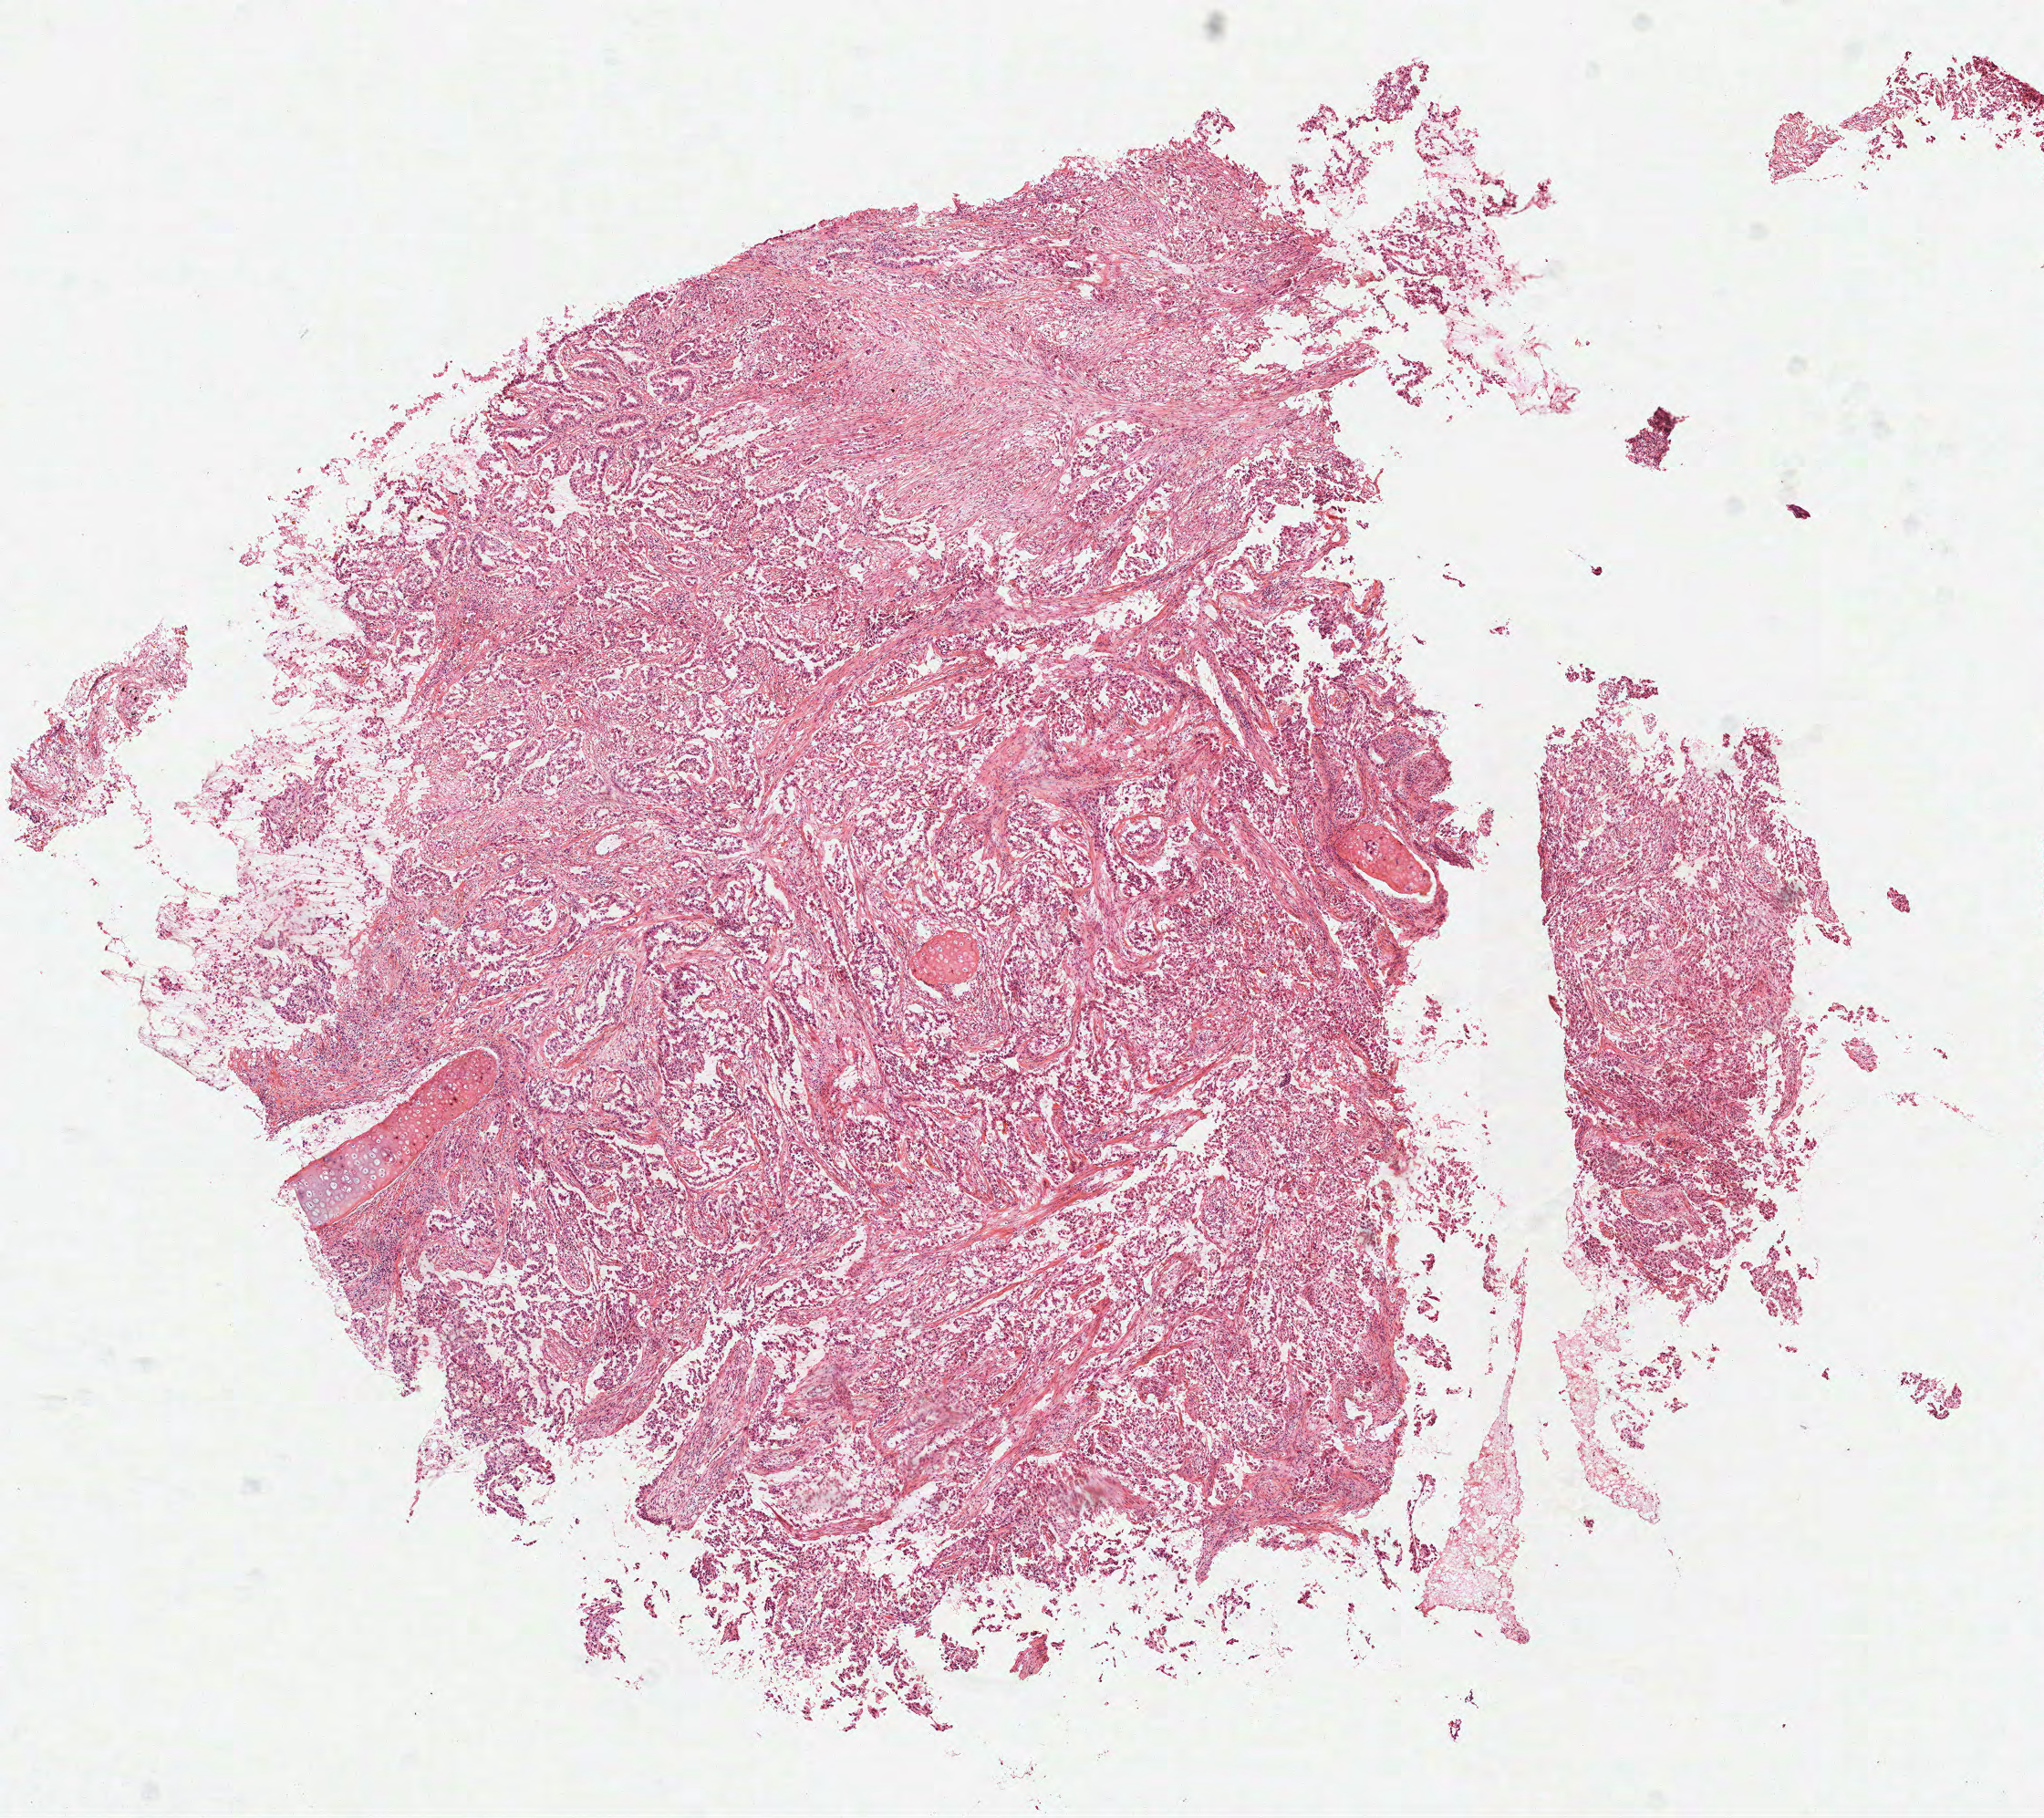
Whole-slide histology image, Hematoxylin and eosin (H&E) stained, a low-resolution overview of the entire scanned area, about 9.0 x 8.0 mm, frozen section, sample: primary tumour, lung. Female, age 60 years at initial diagnosis. Composition of this section per pathologist review: tumour cells 85%, tumour nuclei 80%, normal cells 0%, stromal cells 15%, necrosis 0%.
Pathologic diagnosis: Adenocarcinoma, NOS (upper lobe, lung). TNM: T2 N0 M0. Laterality: left. AJCC pathologic stage: IB (7th edition).